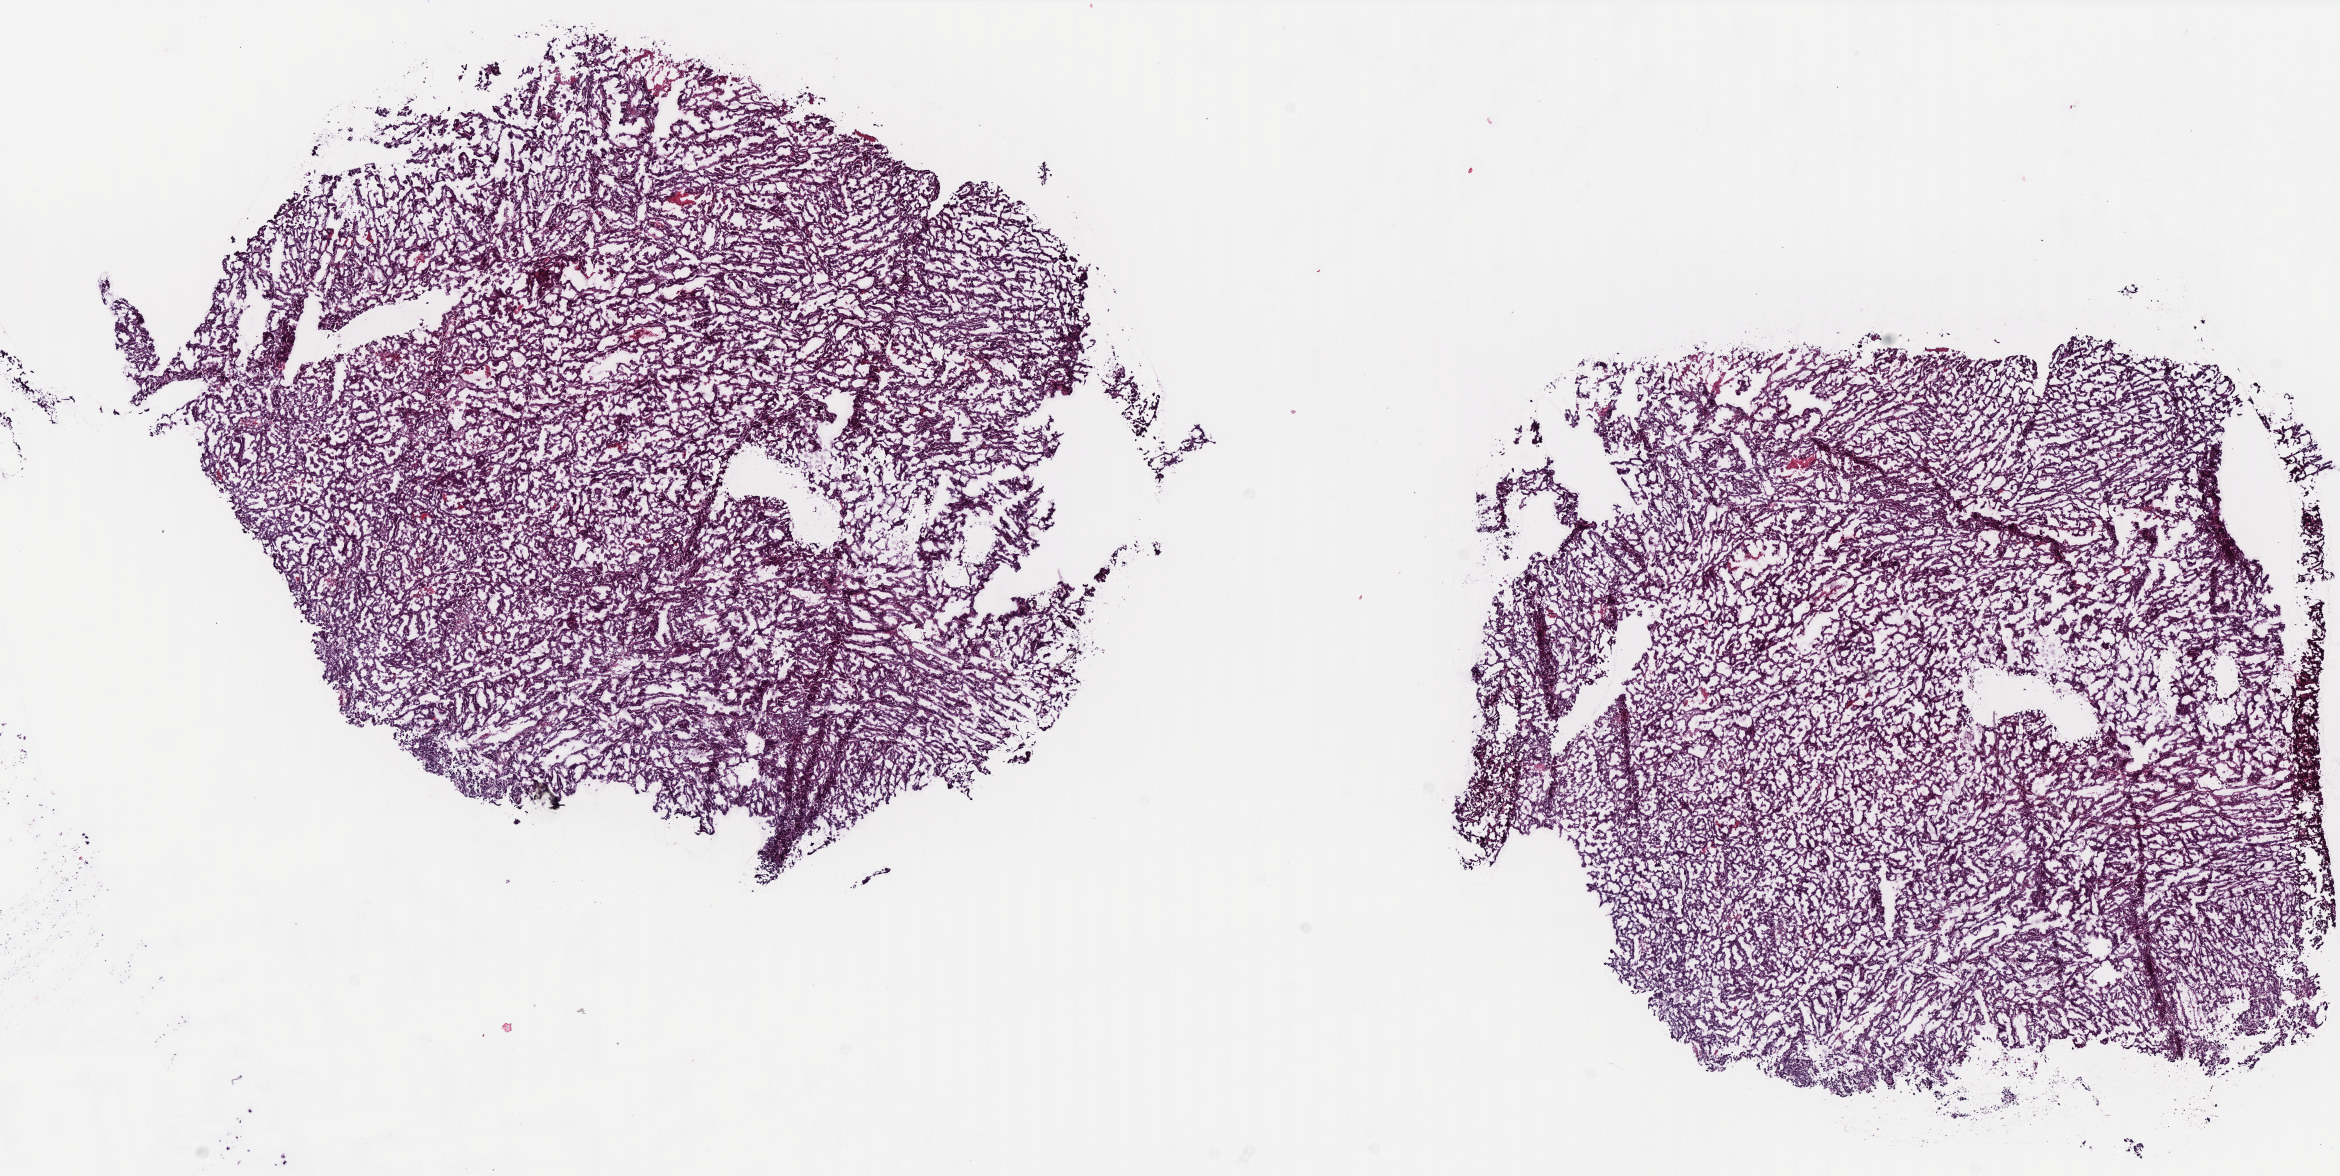
Whole-slide histology image, H&E-stained, a low-resolution overview of the entire scanned area, about 18.8 x 9.4 mm (slide scanned at 40x), frozen section from the top of the tissue portion, sample: primary tumour, uterus. Female patient; age at initial diagnosis 66 years. Pathologist review of this section (percent, as recorded): tumour cells 90%, tumour nuclei 95%.
Pathologic diagnosis: Serous cystadenocarcinoma, NOS (endometrium).